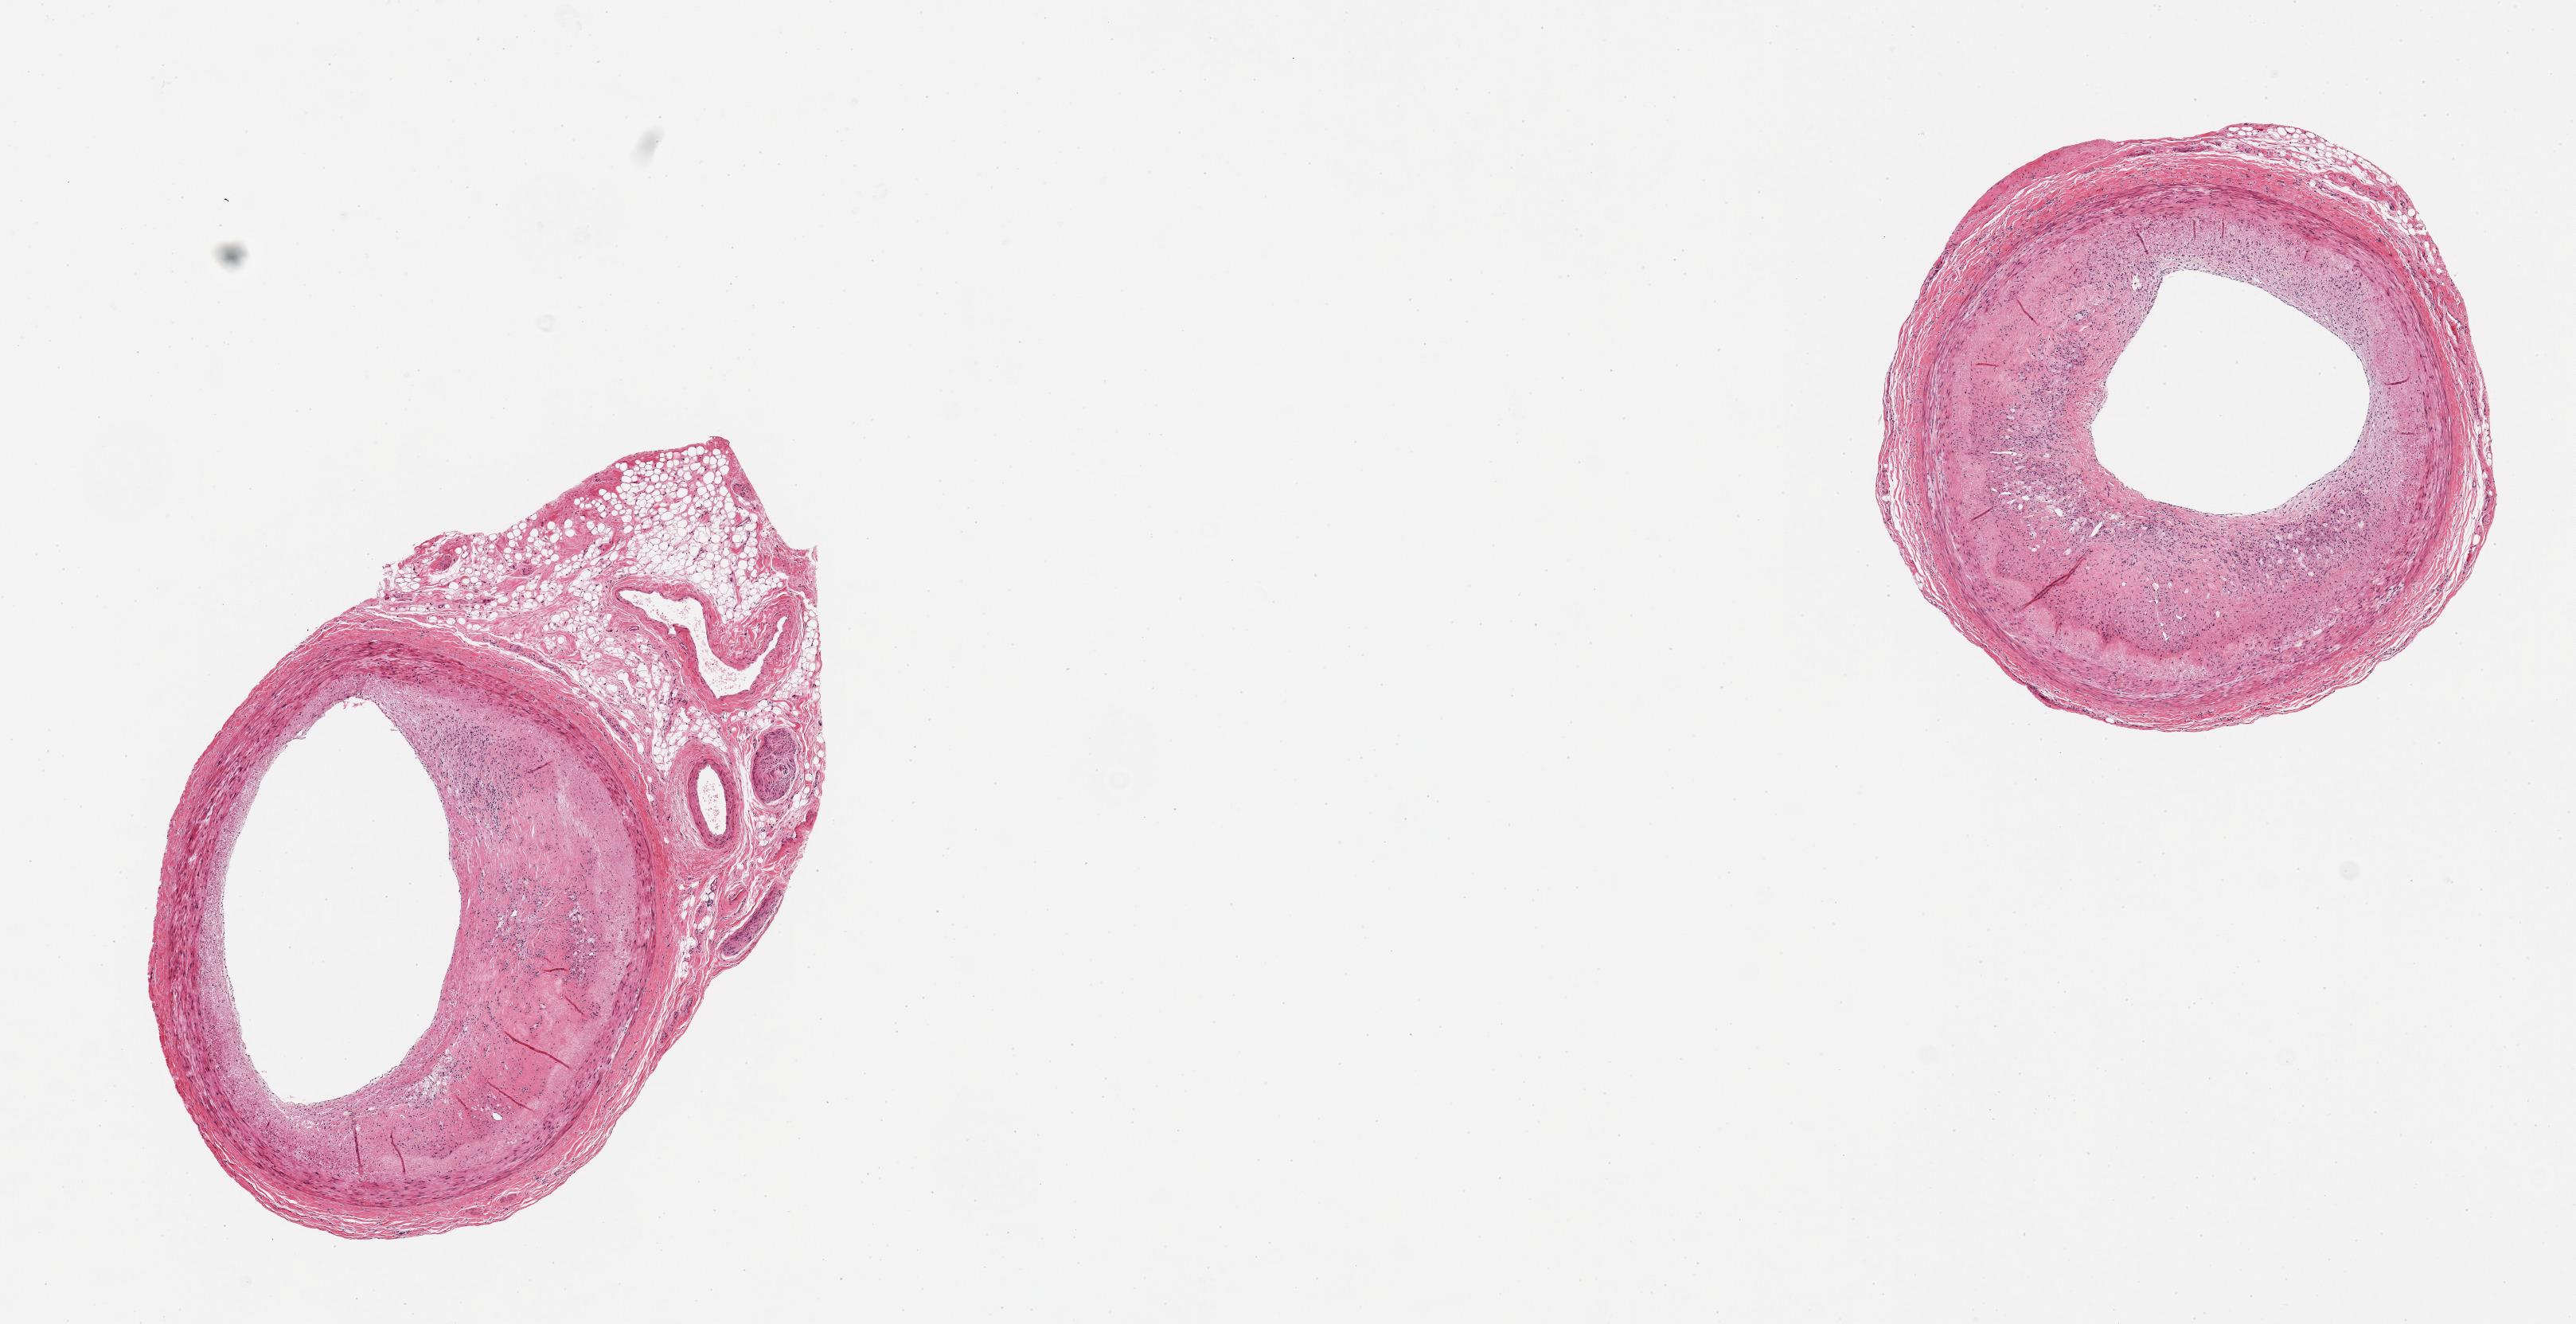
Digitized haematoxylin and eosin-stained section — whole scanned area (about 12.8 x 6.6 mm, acquisition: 20x scan) shown as a low-resolution overview. PAXgene-fixed, paraffin-embedded tissue. Section of coronary artery (target tissue). Tissue donor sample. Male donor.
Reviewer comment on this tissue sample: pieces.